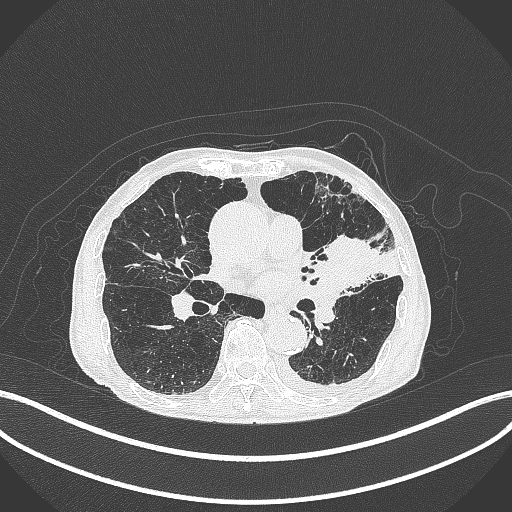
Chest CT, one axial slice. Slice 195 of 385 in the series (ordered by position). 120 kVp. Lung window (W 1500 / L -600 HU). 1 mm slice thickness. 512 × 512 image matrix, field of view 400 × 400 mm. Patient: male, 90 years or older. Case-level facts recorded for this patient, not image findings: clinical TNM (as recorded): T2b N1 M0.
Annotated regions visible in this slice (rectangle marked by the reading radiologist):
- lung tumour (recorded histology: squamous cell carcinoma): bounding box [x1, y1, x2, y2] px = [317, 232, 375, 289]